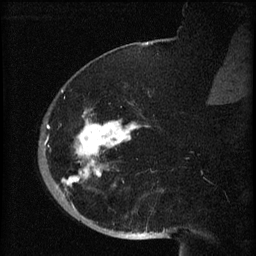
Breast MRI (dynamic contrast-enhanced), one sagittal slice. Position 18 of 60 along the scan axis. Dynamic contrast-enhanced series, image 2 of 3 at this slice position (ordered by acquisition). 1.5 T. TE 4.2 ms, TR 8.2 ms. 2 mm slice thickness. 256 × 256 image matrix, field of view 180 × 180 mm. Patient: female, 71 years.
Outlined on this slice (semi-automatic segmentation, software-assisted and operator-edited):
- analysis volume of interest (the breast-tissue region the enhancement analysis was run in; not a lesion): bounding box [x1, y1, x2, y2] px = [40, 72, 148, 196]
- tumour enhancement mask (voxels above the 70 % enhancement threshold inside the analysis volume of interest): [44, 90, 139, 186]